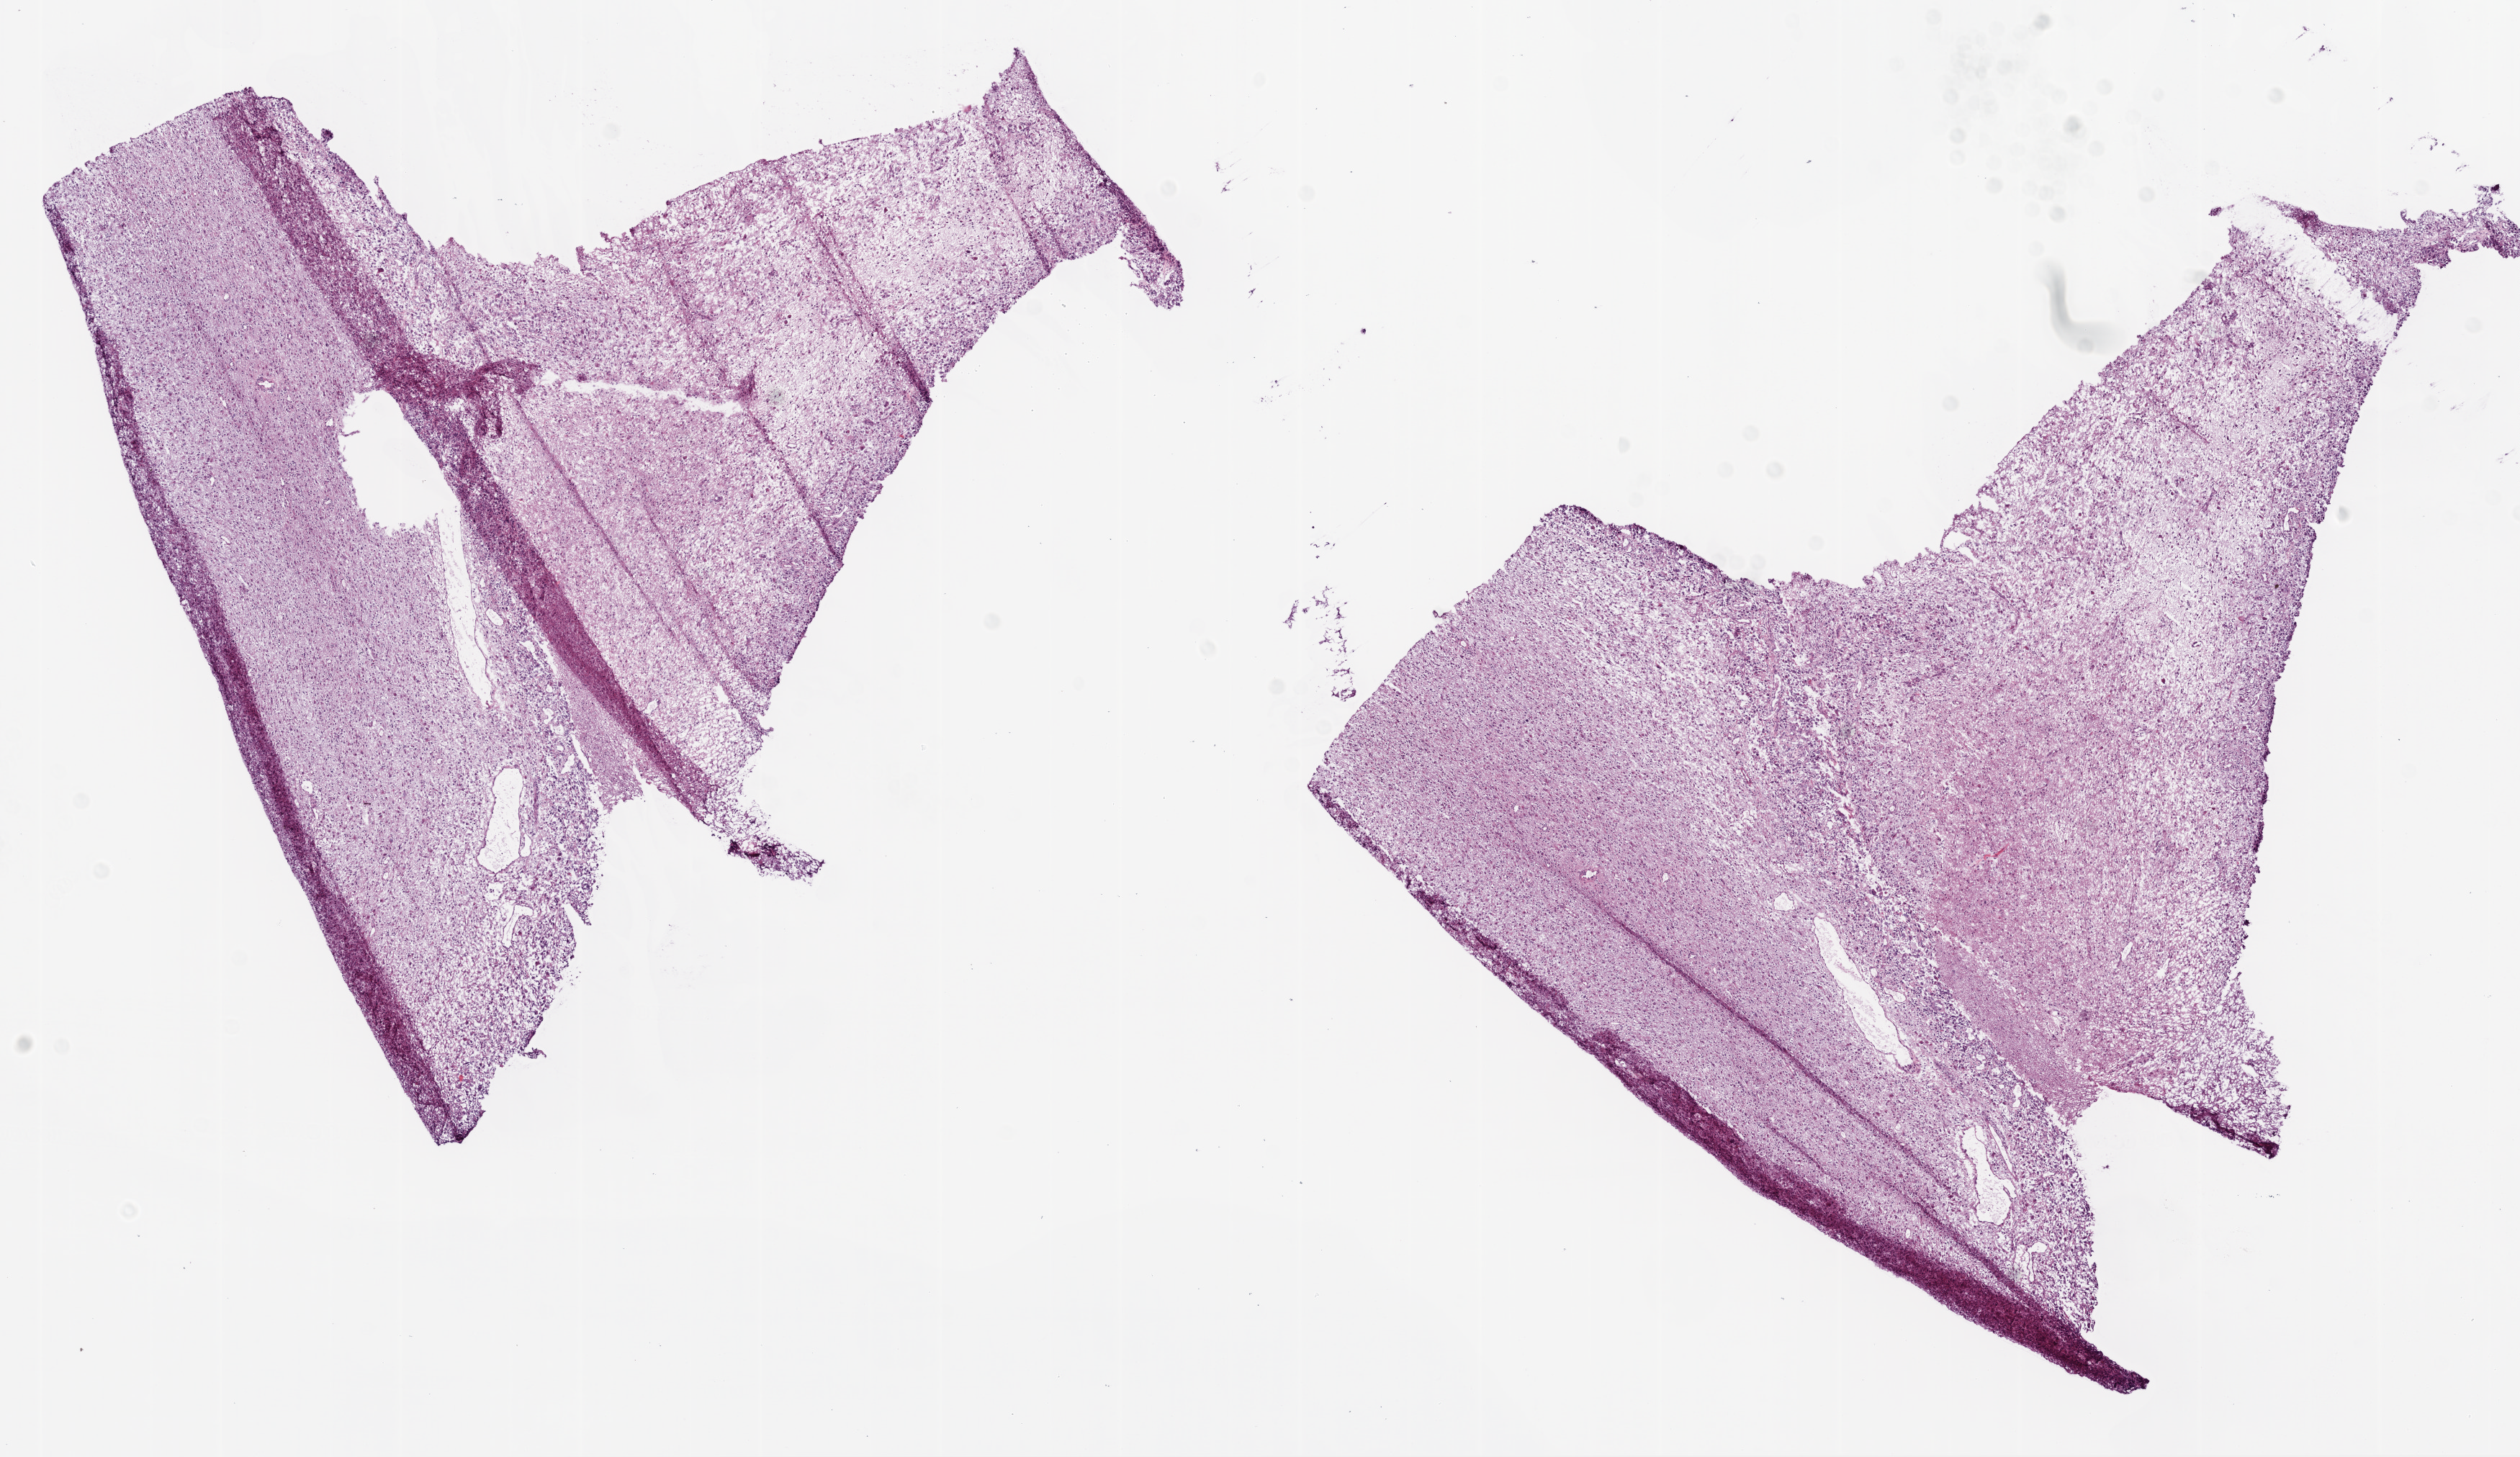
Digitized Hematoxylin and eosin (H&E) stained tissue section (whole slide) — shown as a low-resolution overview of the whole scanned area (about 14.0 x 8.1 mm); frozen section from the top of the tissue portion; brain, primary tumour sample. Patient: female, age at initial diagnosis 42 years. Slide review estimates, as recorded: tumour cells 80%, tumour nuclei 80%, normal cells 10%, stromal cells 10%, necrosis 0%.
* histologic diagnosis: Glioblastoma